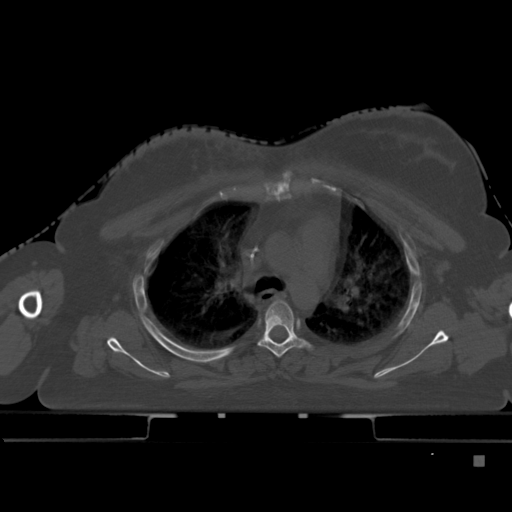
CT including the spine, one axial slice; position 333 of 495 along the scan axis; bone window (W 1800 / L 400 HU); 1.5 mm slice thickness; 512 × 512 image matrix, field of view 404 × 404 mm. Patient: female, 33 years. From the clinical record (not read from this slice): primary cancer: breast; vertebrae with lytic lesions (as recorded): T1.
Annotated regions visible in this slice (semi-automatic segmentation, software-assisted and operator-edited):
- T4 vertebra: bounding box (x1, y1, x2, y2) in pixels: (258, 300, 310, 358)